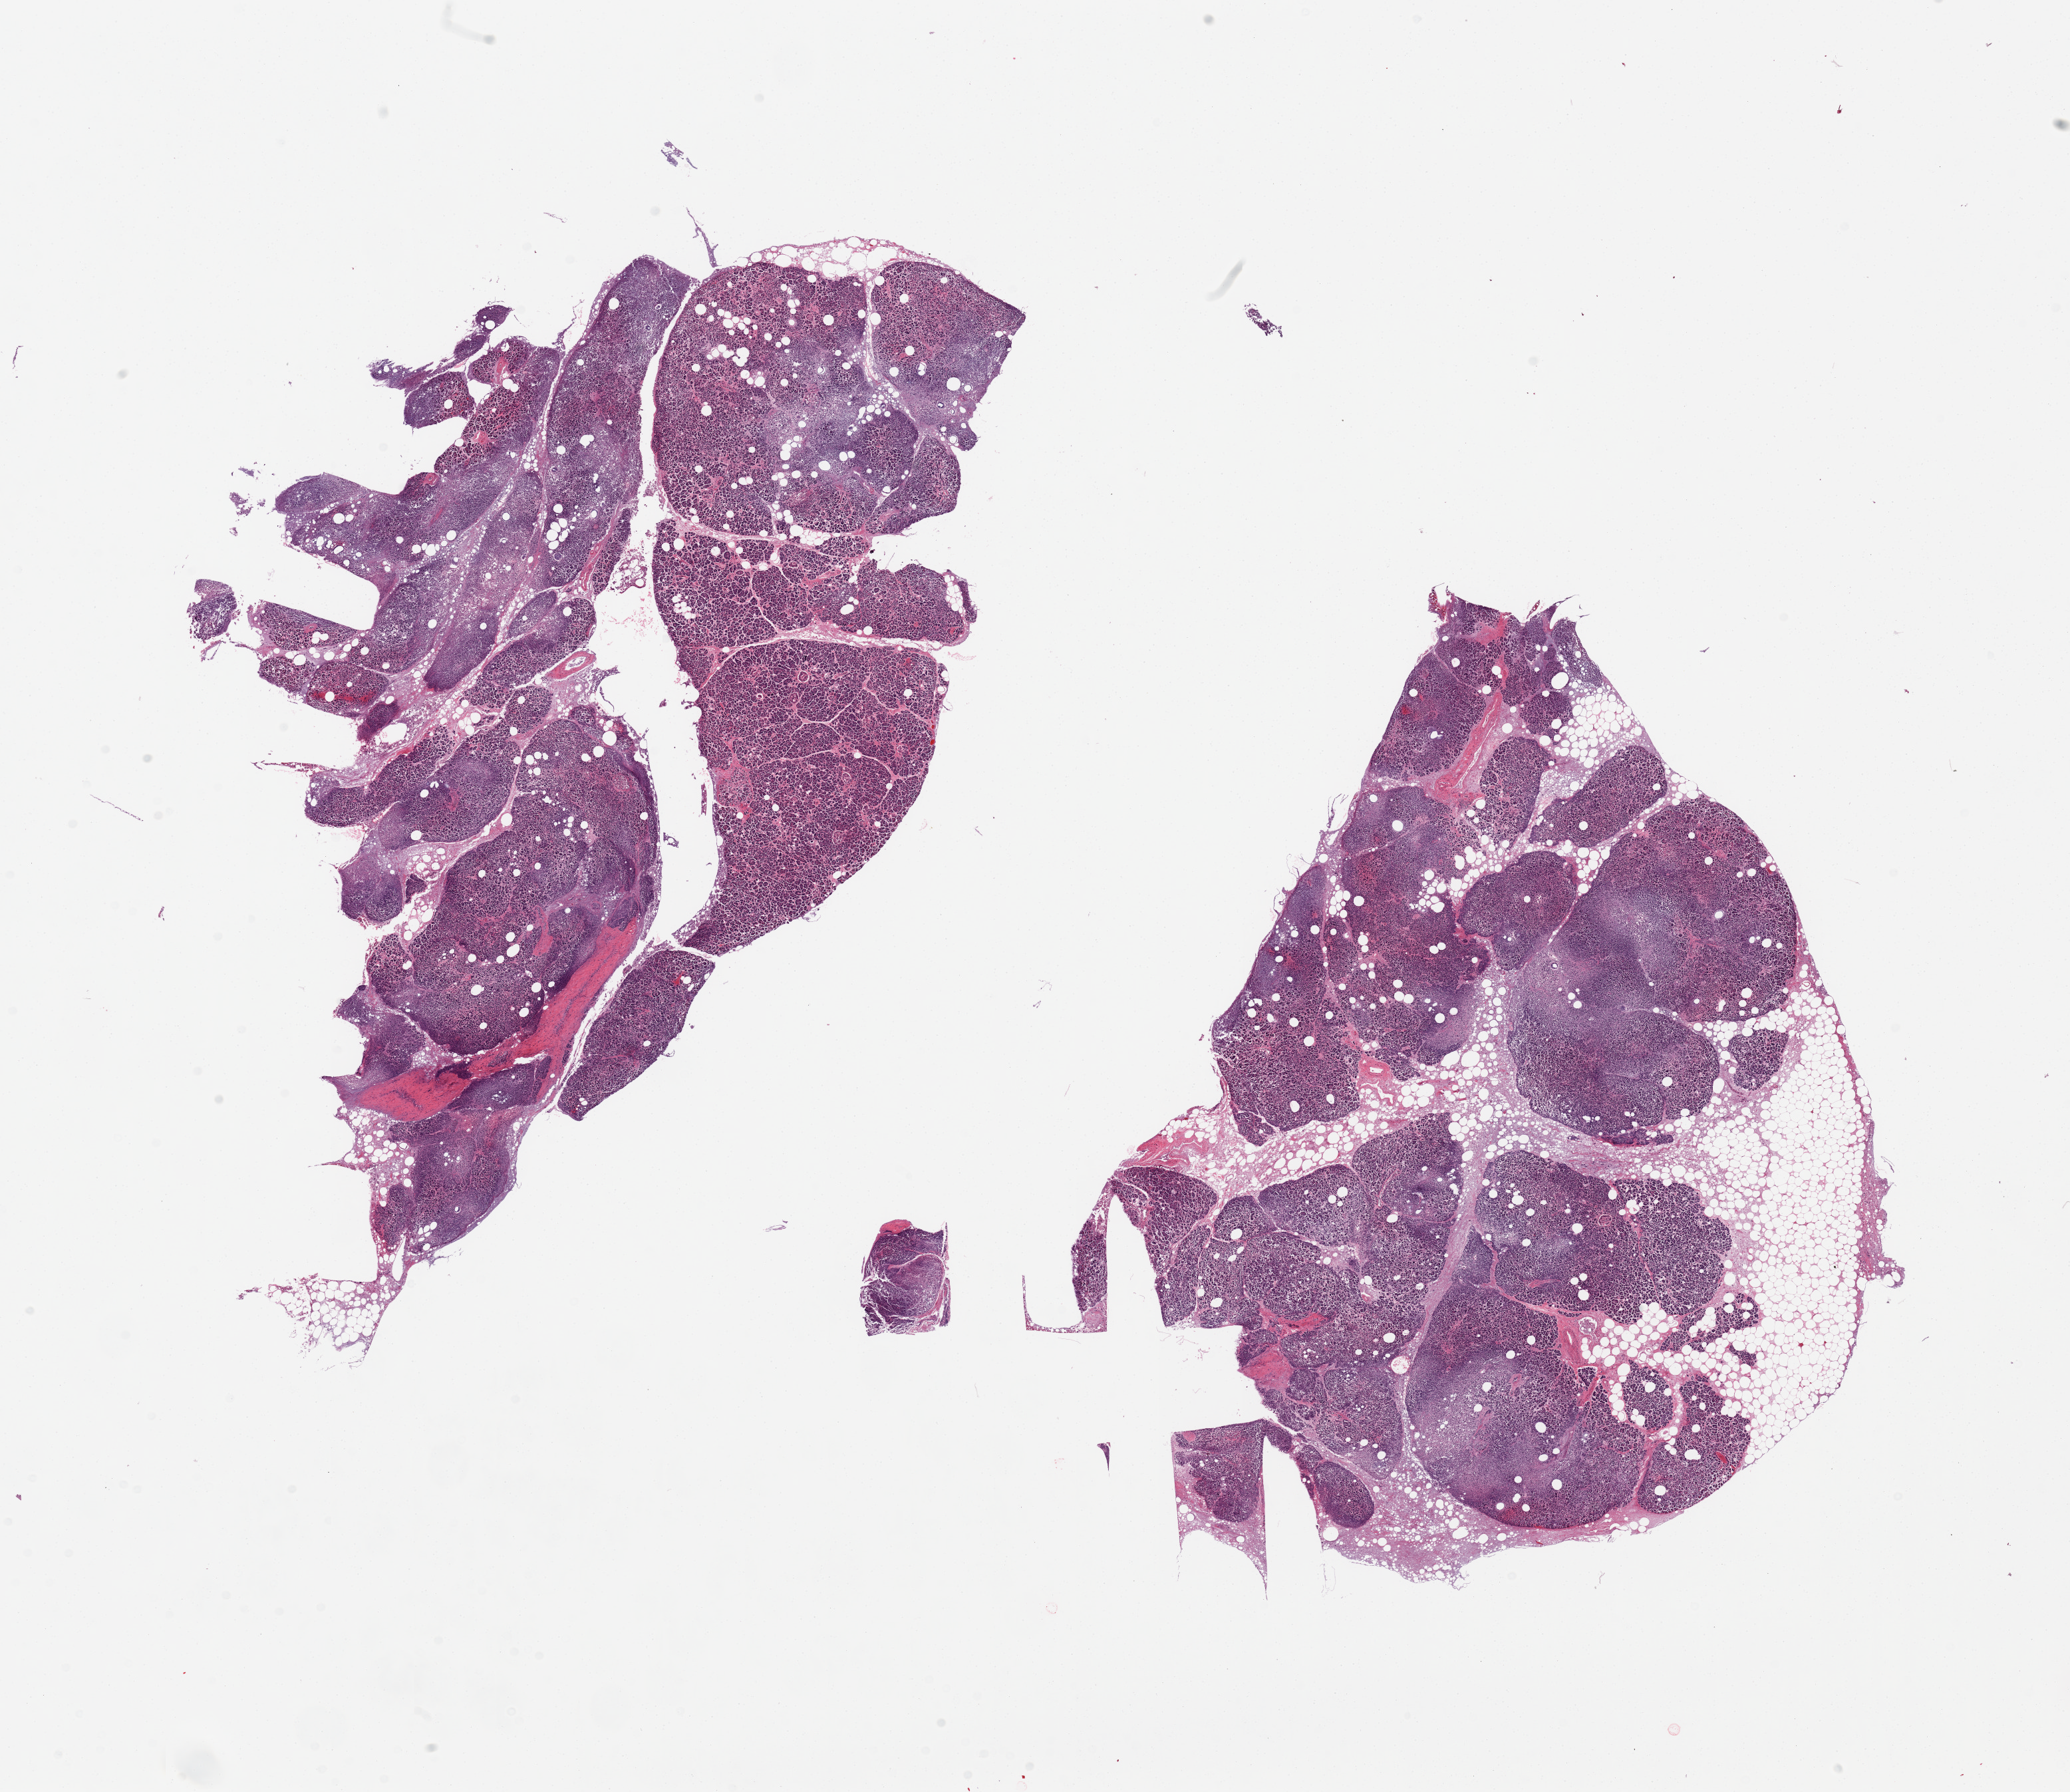
Digitized hematoxylin and eosin (H&E)-stained section, whole scanned area (about 24.6 x 21.3 mm, from a 20x scan) shown as a low-resolution overview. PAXgene-fixed paraffin-embedded (PFPE) section. Section of pancreas (target tissue). Donor tissue sample. Donor sex: male.
Review note (as recorded): 2 pieces, ~30% of one piece is fat, islets seen, marked autolysis/saponification.